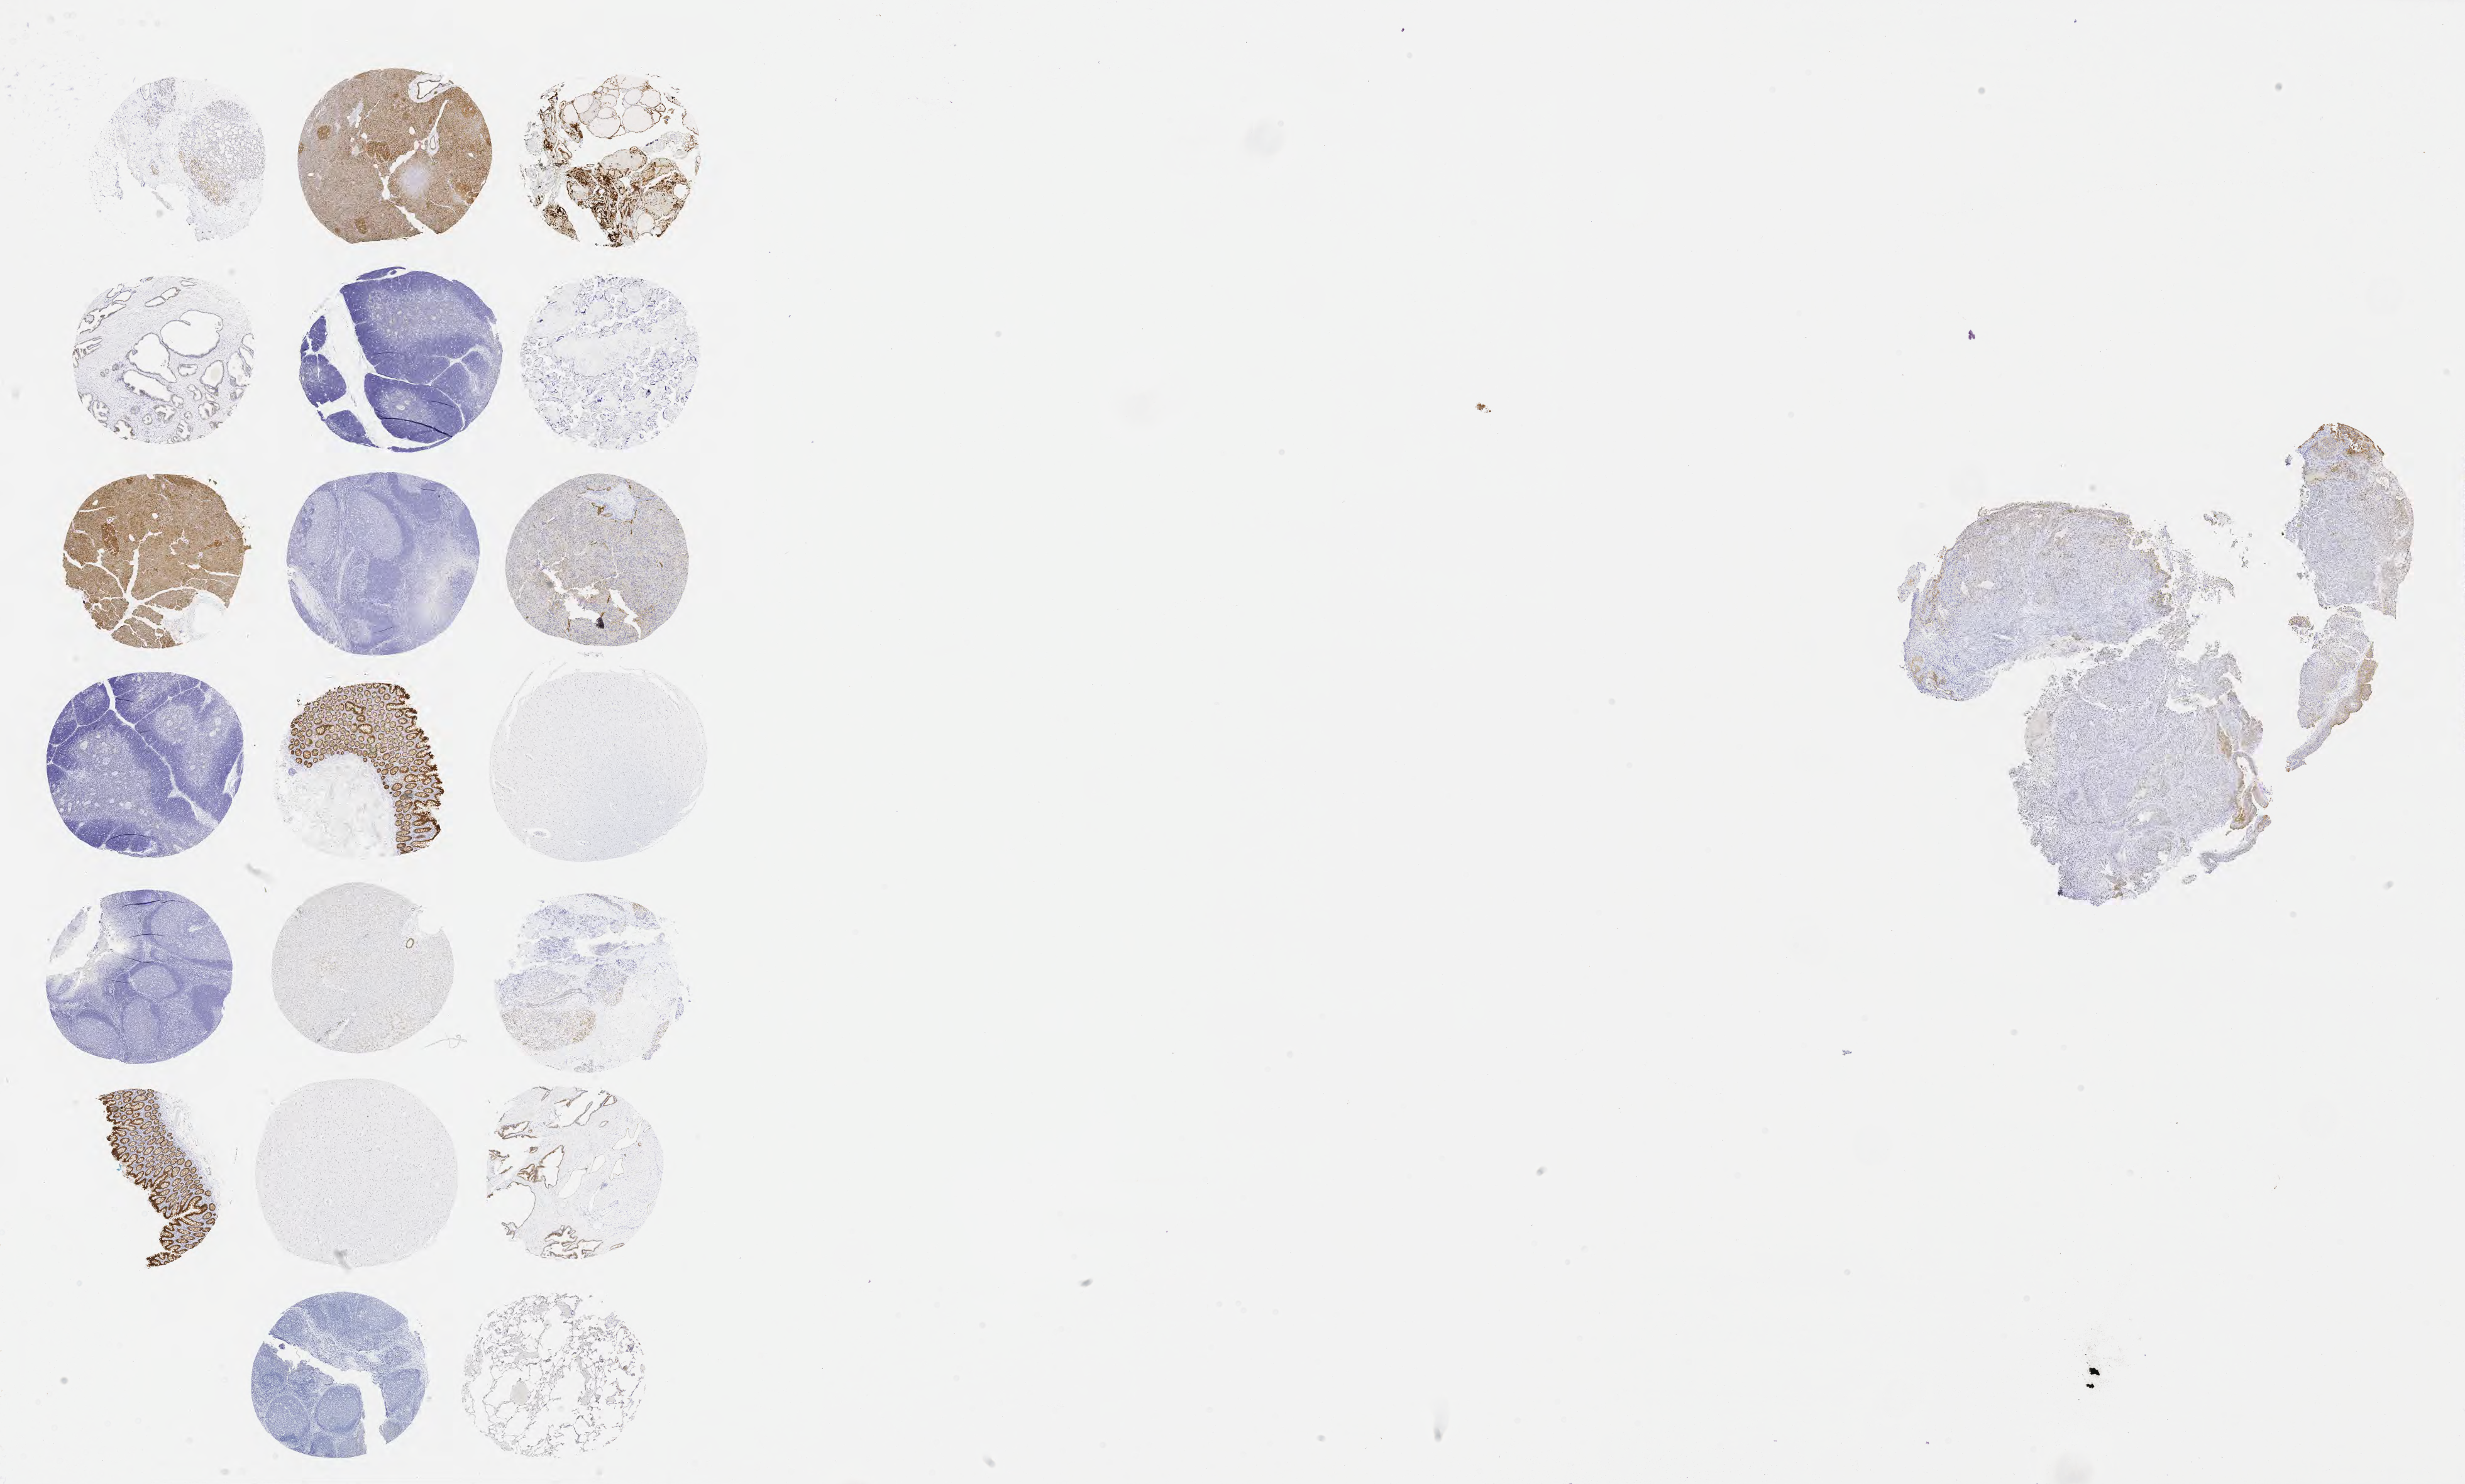
IHC for MOC-31 (anti-EpCAM), whole-slide image, low-resolution overview of the scanned area, about 31.7 x 19.1 mm. Specimen: tumor tissue. Site: cervix. Female patient, age 56 years.
- histologic diagnosis: Adenocarcinoma, NOS